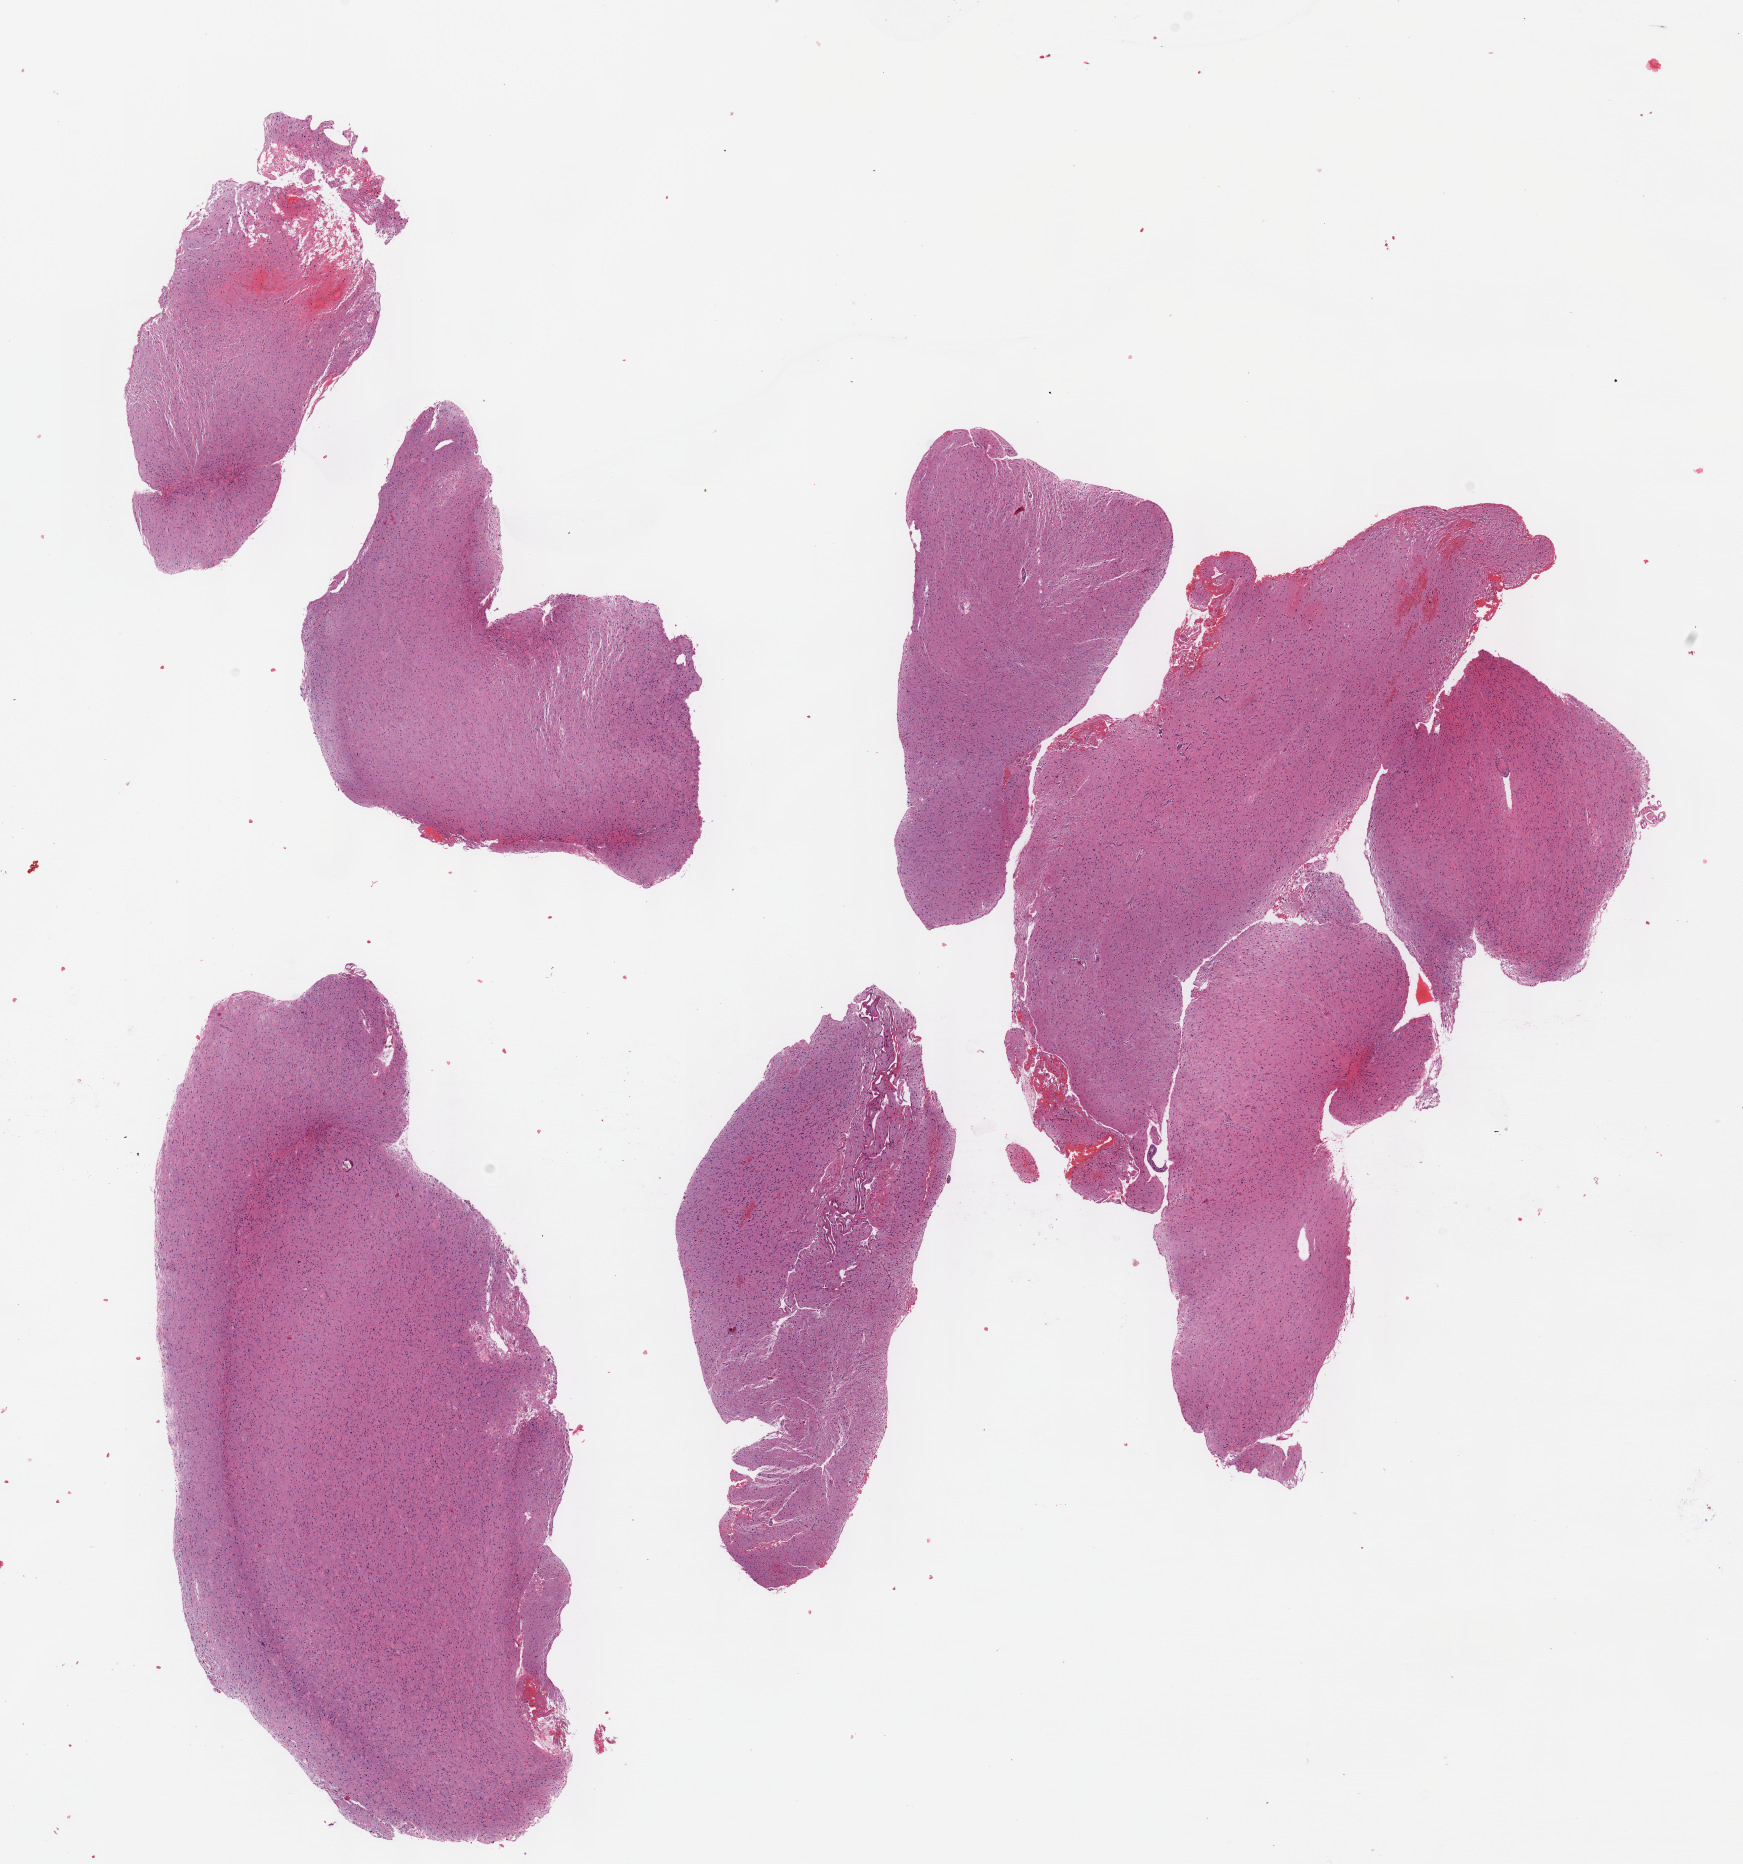
Hematoxylin and eosin (H&E) stained whole-slide image — whole scanned area (about 14.1 x 15.1 mm) shown as a low-resolution overview. FFPE section. Primary tumour sample from the brain. Patient: female, age at initial diagnosis 37 years. Histologic grade: G3 (poorly differentiated).
Histologic diagnosis: Astrocytoma, anaplastic (cerebrum).